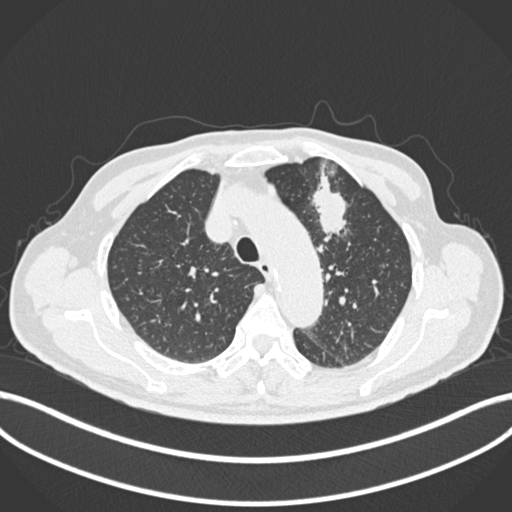
Chest CT, one axial slice. Position 191 of 261 along the scan axis. Reconstruction kernel B30f. 120 kVp. Lung window (W 1500 / L -600 HU). 1 mm slice thickness. 512 × 512 image matrix. Patient: male, 74 years. Case-level facts recorded for this patient, not image findings: clinical TNM (as recorded): T2b N0 M1c.
Outlined on this slice (rectangle marked by the reading radiologist):
- lung tumour (recorded histology: adenocarcinoma): box from (x=305, y=168) to (x=355, y=245) px